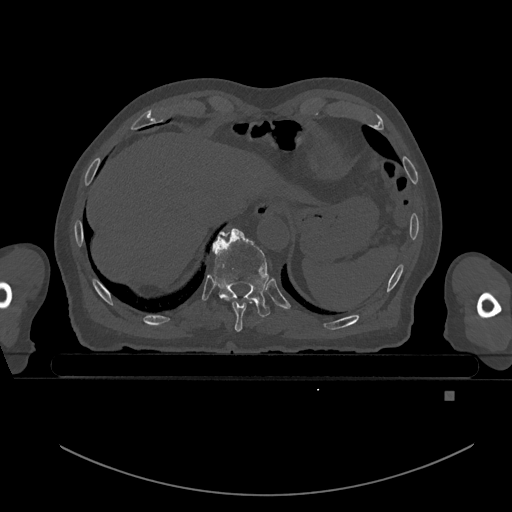
CT including the spine, one axial slice; slice 111 of 969 in the series (ordered by position); bone window (W 1800 / L 400 HU); 0.5 mm slice thickness; 512 × 512 image matrix, field of view 456 × 456 mm. Patient: male, 82 years. Case-level facts recorded for this patient, not image findings: primary cancer: prostate; vertebrae with lytic lesions (as recorded): T11, T9, T8, T2.
Outlined on this slice (semi-automatic segmentation, software-assisted and operator-edited):
- T10 vertebra: bounding box <212,228,270,317> (left, top, right, bottom; pixels)
- T9 vertebra: <219,233,247,332>